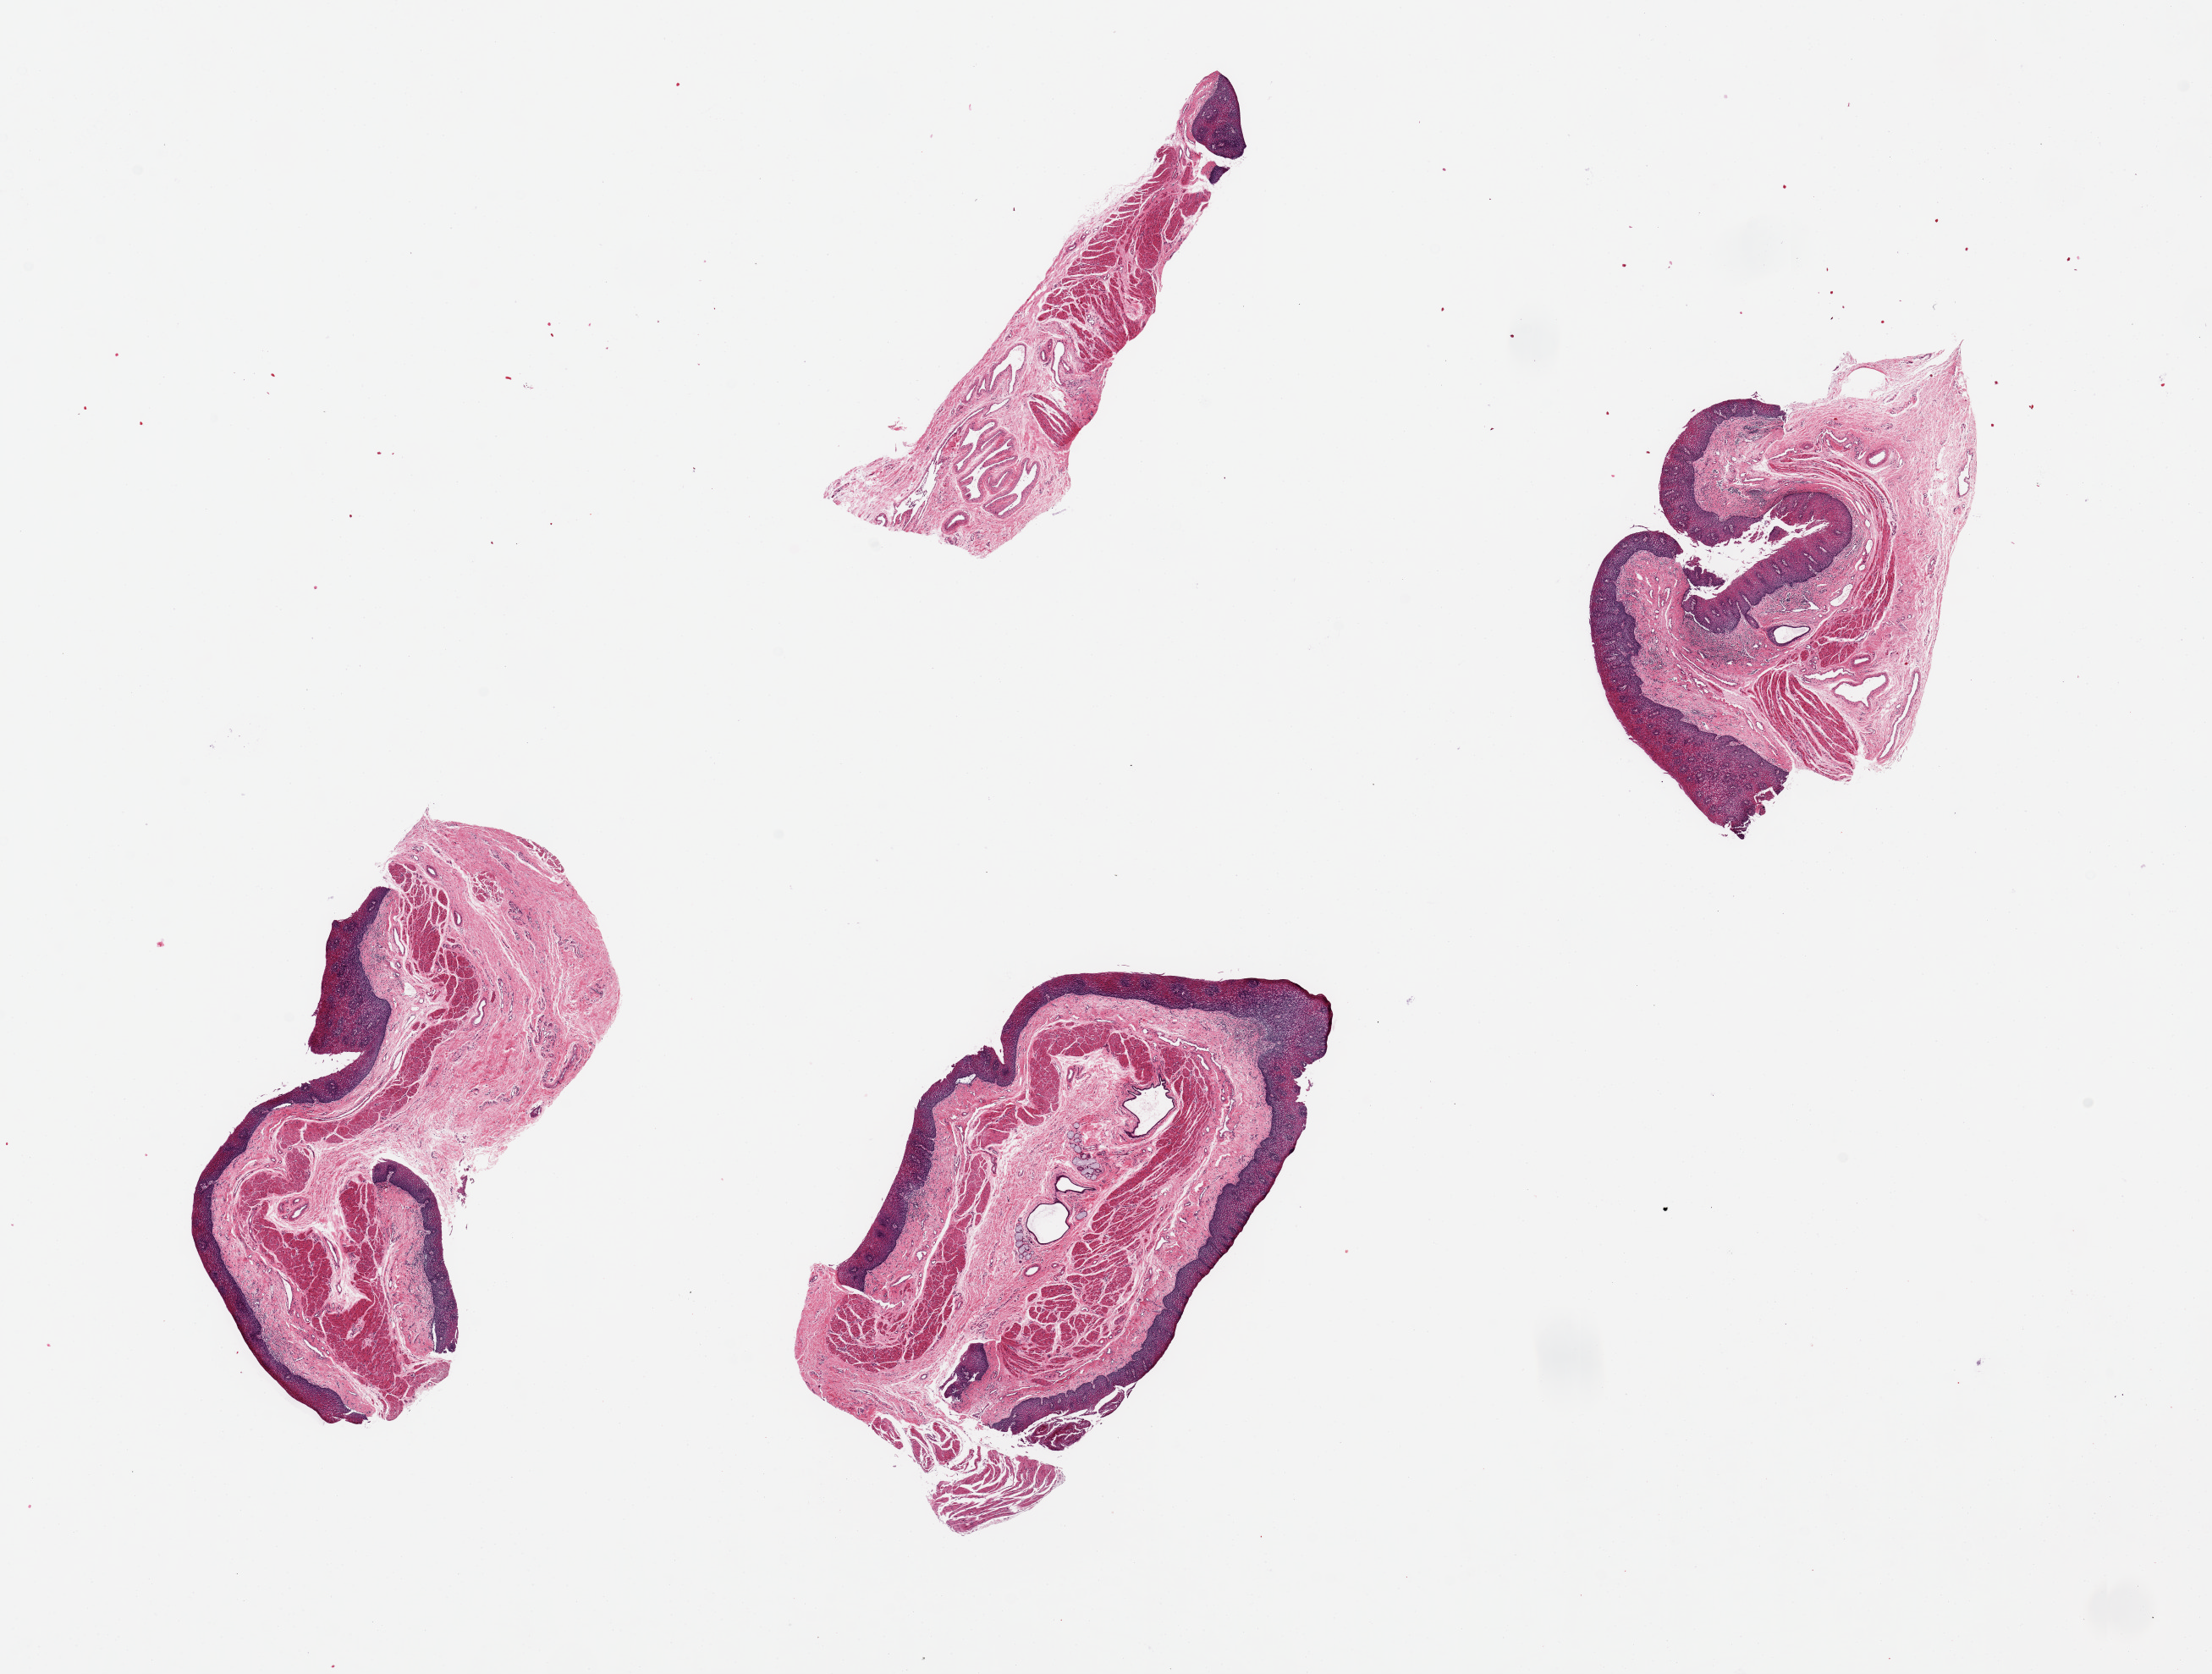
Whole-slide image, hematoxylin and eosin (H&E) stain, brightfield, whole scanned area (about 20.7 x 15.6 mm, slide scanned at 20x) shown as a low-resolution overview. PAXgene-fixed, paraffin-embedded tissue. Sampled site (target tissue): esophageal mucous membrane. Tissue donor sample. Donor: female.
Reviewer comment on this tissue sample: 4 pieces, up to 6x3mm; ~10% squamous mucosa by thickness.